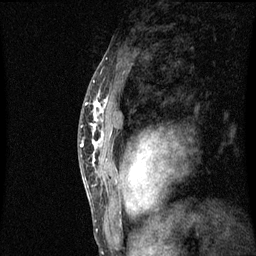
Breast MRI (dynamic contrast-enhanced), one sagittal slice; position 46 of 60 along the scan axis; dynamic contrast-enhanced series, image 2 of 3 at this slice position (ordered by acquisition); 1.5 T; TE 4.2 ms, TR 8.9 ms; 256 × 256 image matrix, field of view 200 × 200 mm. Patient: female, 50 years. From the clinical record (not read from this slice): setting: breast cancer imaged before/during neoadjuvant chemotherapy; receptor status: triple-negative.
Annotated regions visible in this slice (semi-automatically segmented with operator editing):
- analysis volume of interest (the breast-tissue region the enhancement analysis was run in; not a lesion): bounding box [x1, y1, x2, y2] px = [84, 80, 115, 171]
- tumour enhancement mask (voxels above the 70 % enhancement threshold inside the analysis volume of interest): [86, 94, 109, 149]